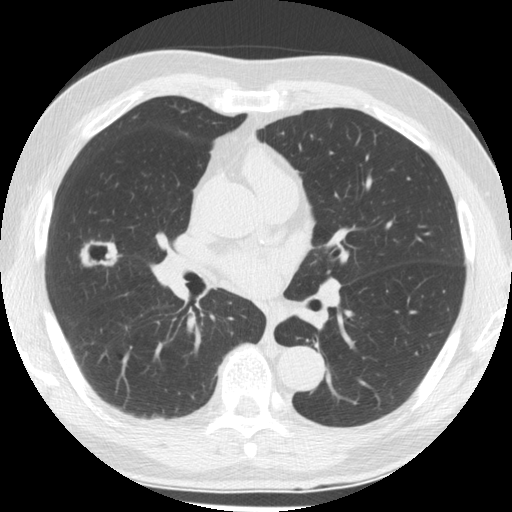
Low-dose screening chest CT, one axial slice; slice 100 of 176 in the series (ordered by position); lung window (W 1500 / L -600 HU); 2.5 mm slice thickness; 512 × 512 image matrix, field of view 348 × 348 mm.
Structures marked on this image (expert manual segmentation):
- lesion 1 (tumor, middle lobe of right lung): bounding box [x1, y1, x2, y2] px = [80, 240, 120, 267]